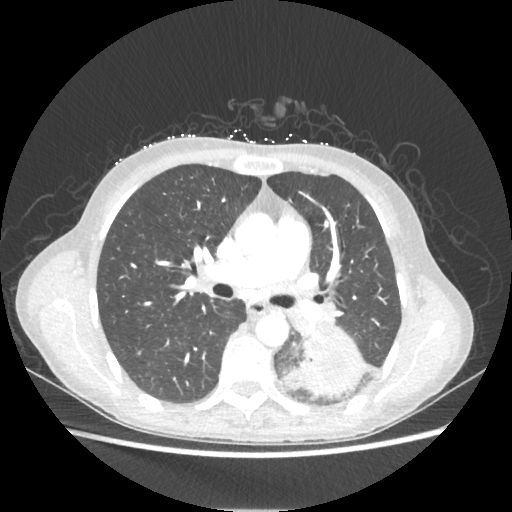
Chest CT, one axial slice; slice 130 of 221 in the series (ordered by position); reconstruction kernel STANDARD; lung window (W 1500 / L -600 HU); 1.25 mm slice thickness; 512 × 512 image matrix, field of view 360 × 360 mm. Female patient, age 53 years. Case-level facts recorded for this patient, not image findings: clinical TNM (as recorded): T3 N0 M0.
Annotated regions visible in this slice (rectangle marked by the reading radiologist):
- lung tumour (recorded histology: adenocarcinoma): bounding box [x1, y1, x2, y2] px = [287, 328, 368, 396]